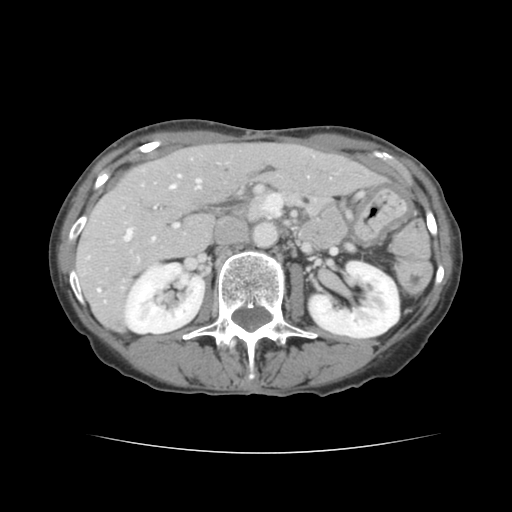
Contrast-enhanced abdominal CT, one axial slice; position 68 of 136 along the scan axis; intravenous contrast given; soft-tissue window (W 400 / L 40 HU); 2.5 mm slice thickness; 512 × 512 image matrix, field of view 319 × 319 mm. Female patient, age 77 years. From the clinical record (not read from this slice): diagnosis: colorectal cancer liver metastases, imaged before liver resection; multiple liver metastases: yes; largest metastasis: 3 cm; disease in both lobes: no.
Annotated regions visible in this slice (outlined manually by an expert reader):
- hepatic veins: bounding box (x1, y1, x2, y2) in pixels: (125, 175, 201, 240)
- liver: (77, 143, 381, 330)
- planned liver remnant (the part of the liver to remain after resection): (159, 144, 380, 204)
- portal vein (with intrahepatic branches): (98, 224, 178, 292)